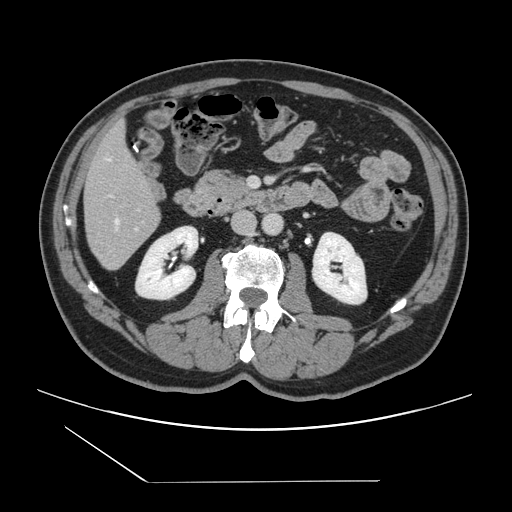
Contrast-enhanced abdominal CT, one axial slice; slice 46 of 157 in the series (ordered by position); 120 kVp; soft-tissue window (W 400 / L 40 HU); 2.5 mm slice thickness; 512 × 512 image matrix, field of view 407 × 407 mm. Male patient, age 61 years. Case-level facts recorded for this patient, not image findings: diagnosis: colorectal cancer liver metastases, imaged before liver resection; multiple liver metastases: yes; largest metastasis: 5.5 cm; disease in both lobes: yes.
Outlined on this slice (expert manual segmentation):
- hepatic veins: bounding box <108,158,120,229> (left, top, right, bottom; pixels)
- liver: <85,125,160,269>
- planned liver remnant (the part of the liver to remain after resection): <85,126,156,218>
- portal vein (with intrahepatic branches): <111,195,139,230>